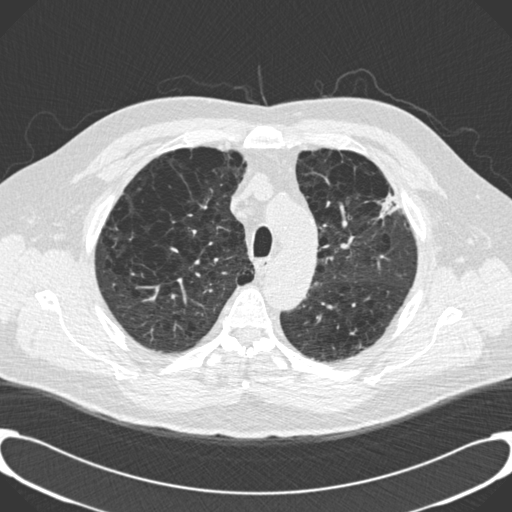
Low-dose screening chest CT, one axial slice. Slice 151 of 189 in the series (ordered by position). 120 kVp. Lung window (W 1500 / L -600 HU). 512 × 512 image matrix, field of view 380 × 380 mm.
Annotated regions visible in this slice (outlined manually by an expert reader):
- lesion 1 (tumor, upper lobe of left lung): bounding box <378,193,403,218> (left, top, right, bottom; pixels)